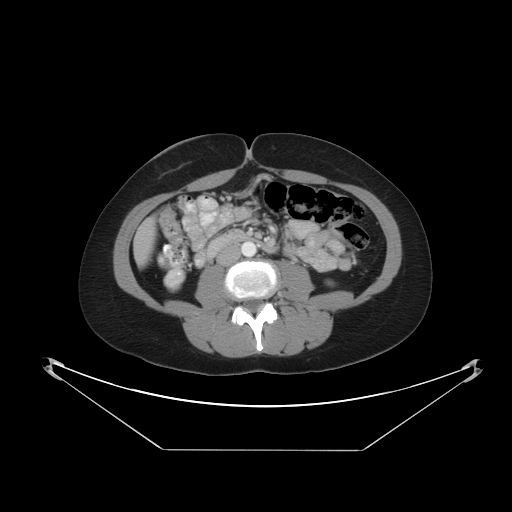
Contrast-enhanced abdominal CT, one axial slice; reconstruction kernel STANDARD; 120 kVp; intravenous contrast given; soft-tissue window (W 400 / L 40 HU); 5 mm slice thickness; 512 × 512 image matrix, field of view 482 × 482 mm. Female patient, age 38 years. Case-level facts recorded for this patient, not image findings: diagnosis: colorectal cancer liver metastases, imaged before liver resection.
Structures marked on this image (outlined manually by an expert reader):
- liver: bounding box [x1, y1, x2, y2] px = [133, 216, 158, 266]